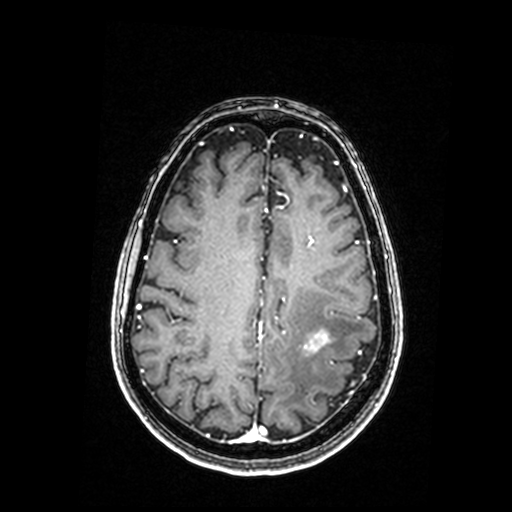
Brain MRI from a brain-tumour surgery series, one axial slice. Slice 65 of 192 in the series (ordered by position). T1-weighted post-contrast. 512 × 512 image matrix, field of view 250 × 250 mm. From the clinical record (not read from this slice): histopathology: Metastastic Carcinoma, Poorly Differentiated; tumour location: Left Parietal.
Outlined on this slice (manually delineated by an expert):
- tumour: bounding box (x1, y1, x2, y2) in pixels: (317, 333, 328, 344)